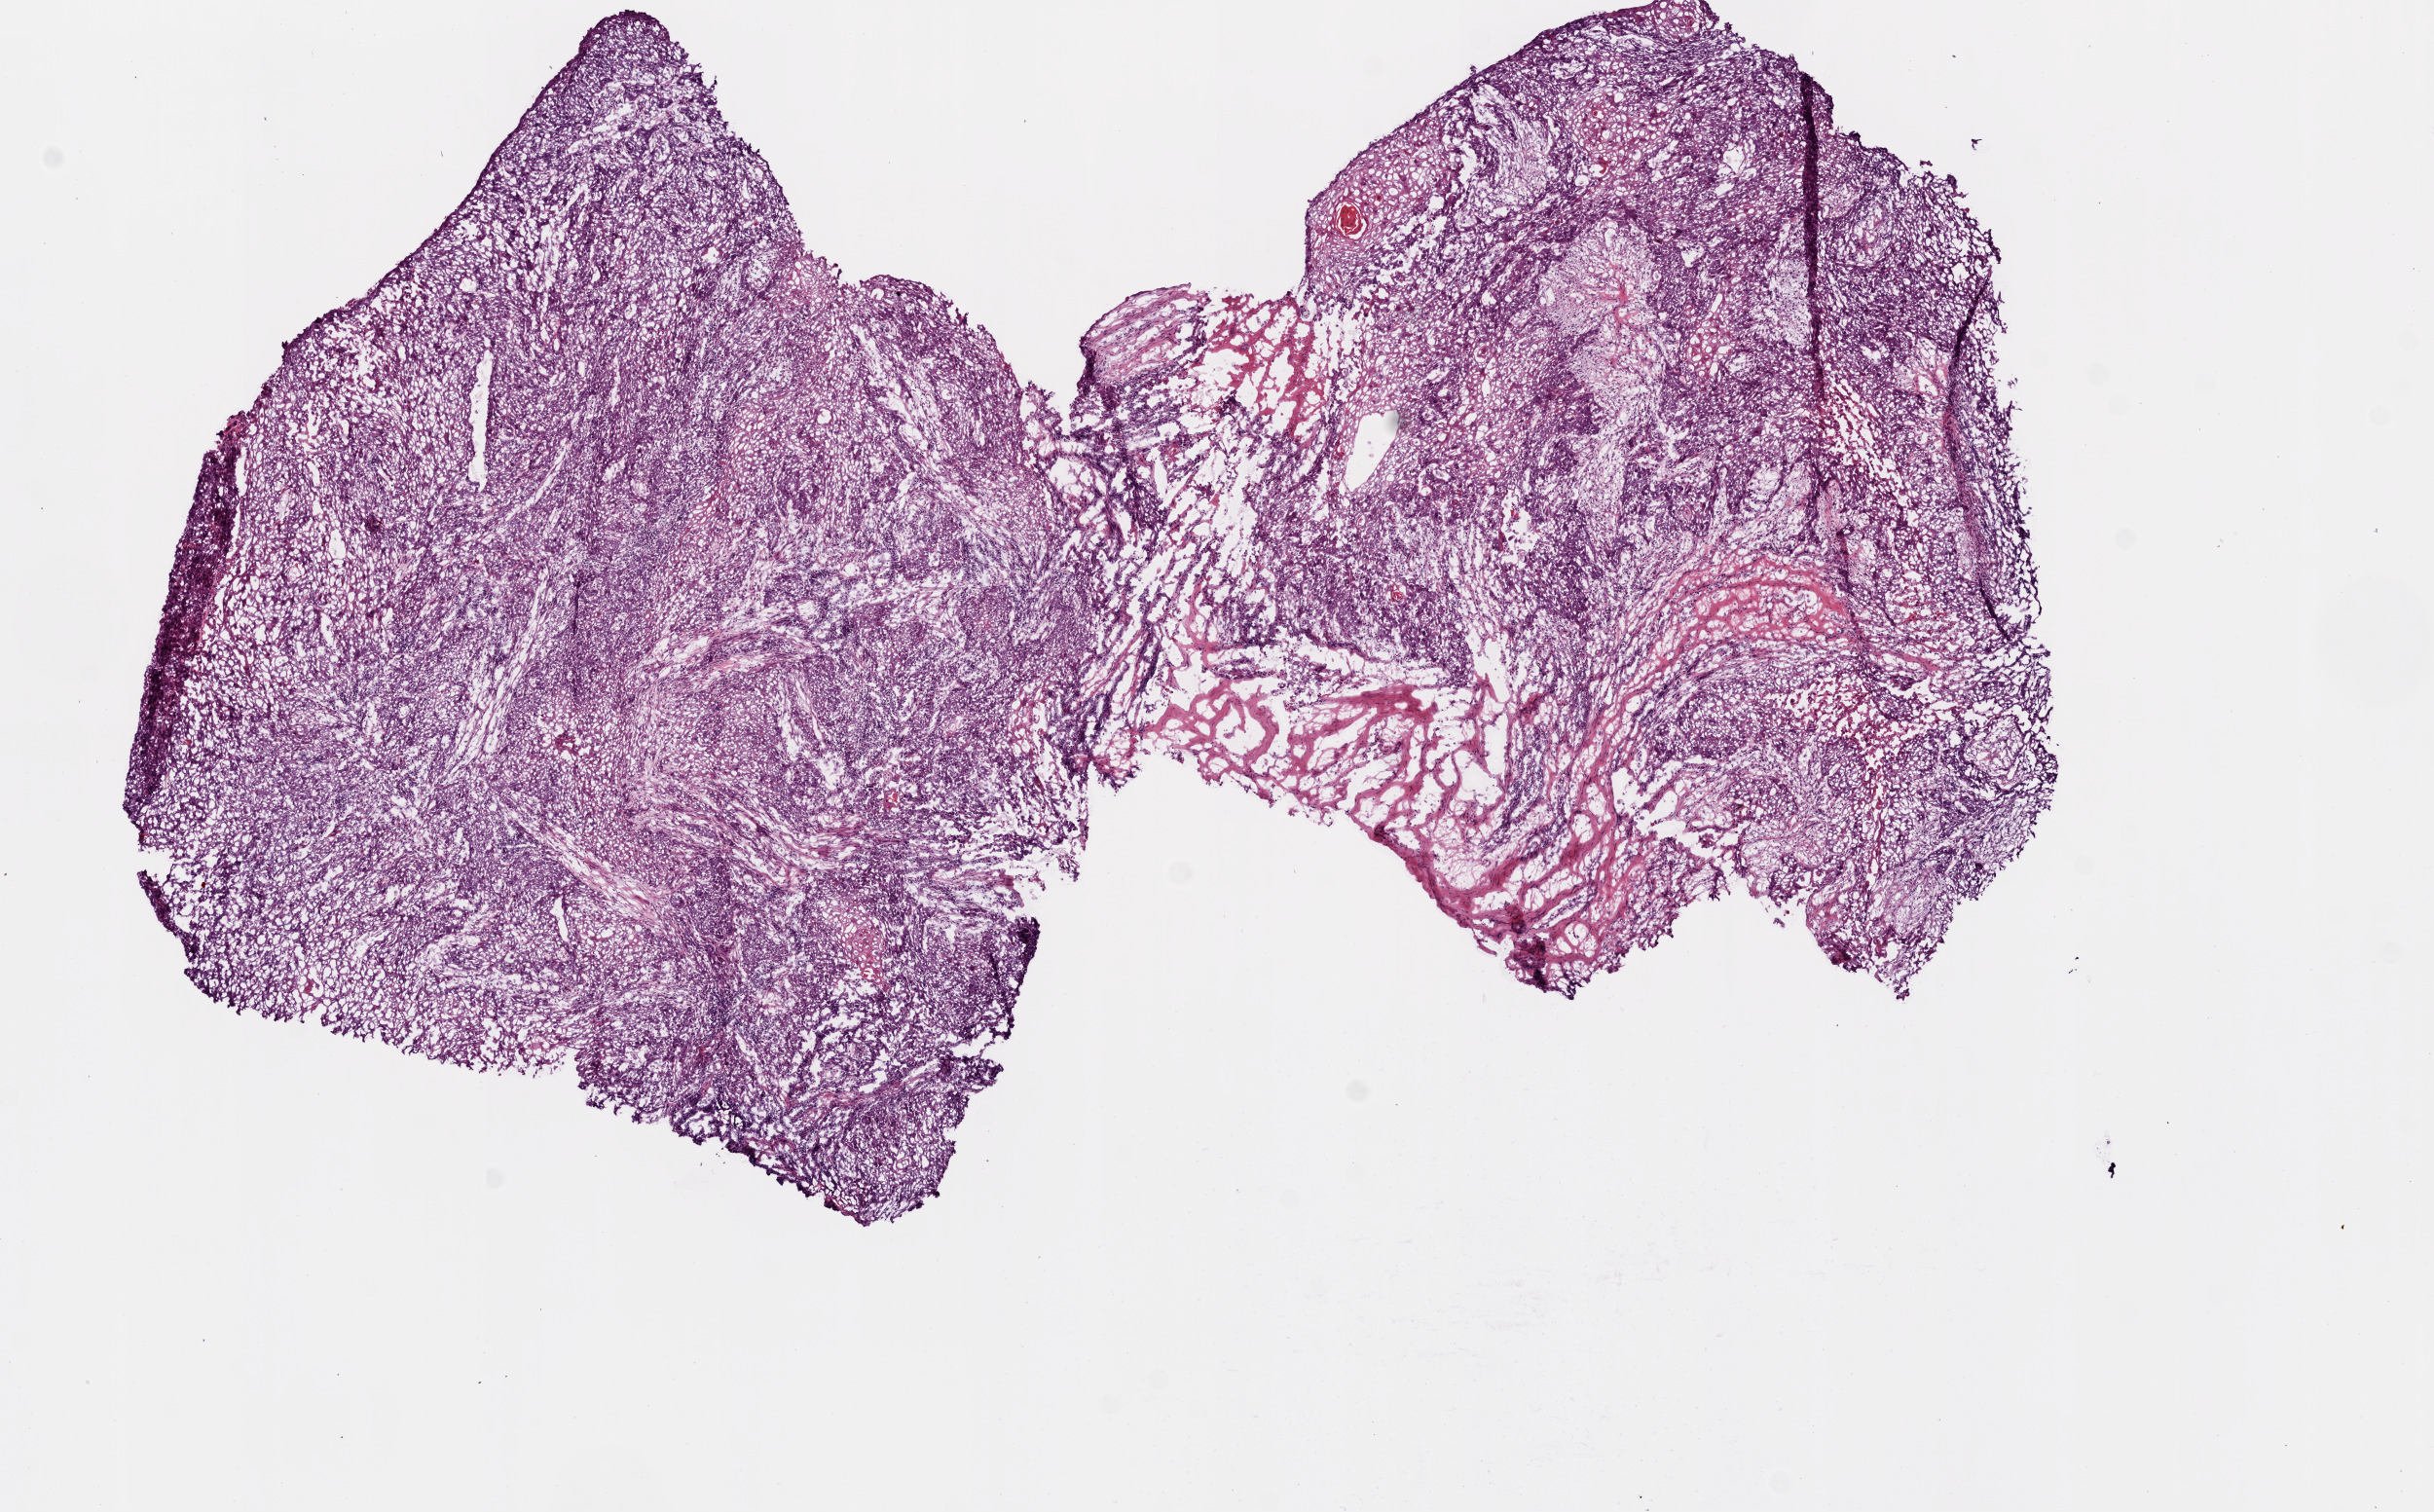
H&E-stained whole-slide image — a low-resolution overview of the entire scanned area, about 10.0 x 6.2 mm. Frozen section from the top of the tissue portion. Sample: primary tumour, head and neck. Patient: male, age at initial diagnosis 67 years. Histologic grade: G2 (moderately differentiated). Pathologist review of this section (percent, as recorded): tumour cells 87%, tumour nuclei 75%, normal cells 0%, stromal cells 10%, necrosis 3%.
AJCC pathologic stage: IVA (7th edition). TNM: T4a N0. Diagnosis: Squamous cell carcinoma, NOS (larynx, NOS).